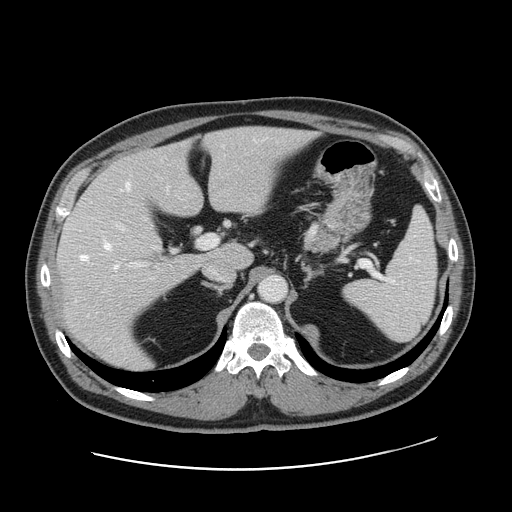
Contrast-enhanced abdominal CT, one axial slice; slice 104 of 178 in the series (ordered by position); intravenous contrast given; soft-tissue window (W 400 / L 40 HU); 2.5 mm slice thickness; 512 × 512 image matrix, field of view 403 × 403 mm. Male patient, age 63 years. Case-level facts recorded for this patient, not image findings: diagnosis: colorectal cancer liver metastases, imaged before liver resection; multiple liver metastases: yes; largest metastasis: 8 cm; disease in both lobes: yes.
Outlined on this slice (manually delineated by an expert):
- hepatic veins: box from (x=81, y=183) to (x=129, y=269) px
- liver: (x=59, y=127)–(x=309, y=370)
- planned liver remnant (the part of the liver to remain after resection): (x=124, y=127)–(x=309, y=267)
- portal vein (with intrahepatic branches): (x=116, y=224)–(x=218, y=266)